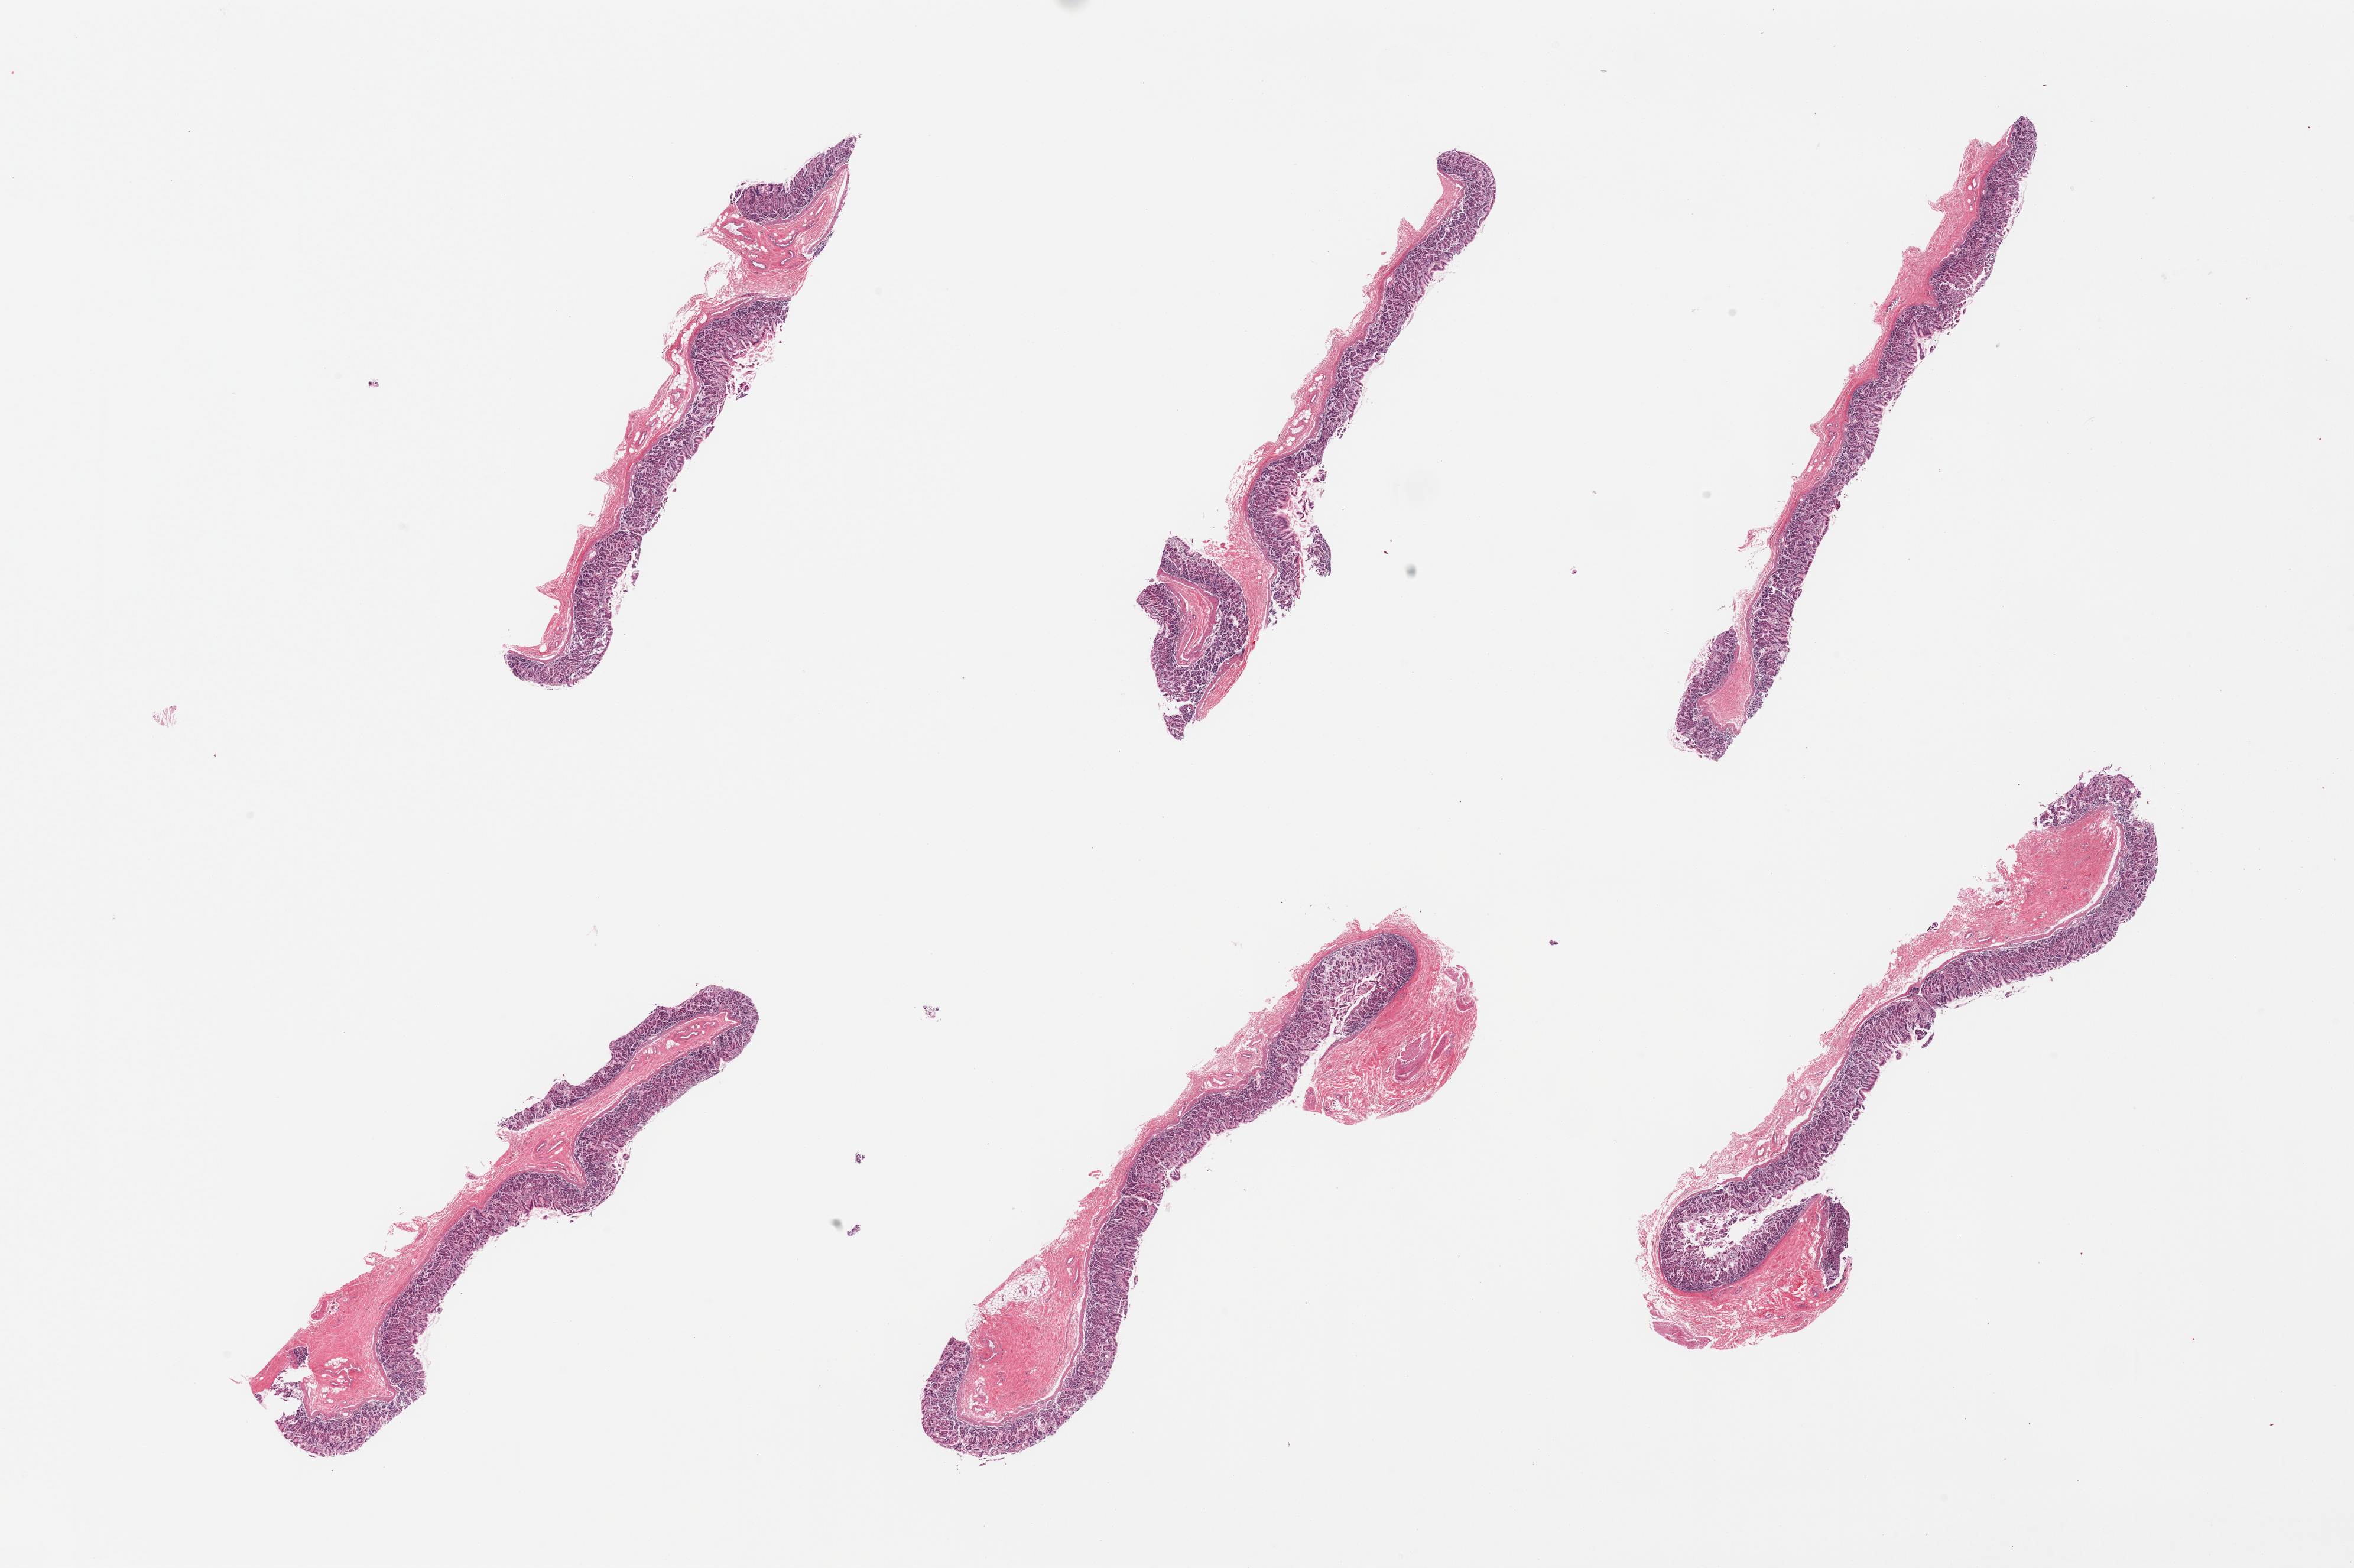
Haematoxylin and eosin whole-slide image, whole scanned area (about 31.5 x 21.0 mm, acquisition: 20x scan) shown as a low-resolution overview. PAXgene-fixed paraffin-embedded (PFPE) section. Sampled site (target tissue): stomach. Donor tissue sample. Female donor.
Pathologist's review note for this sample: 6 pieces, mild chronic gastritis with atrophy.